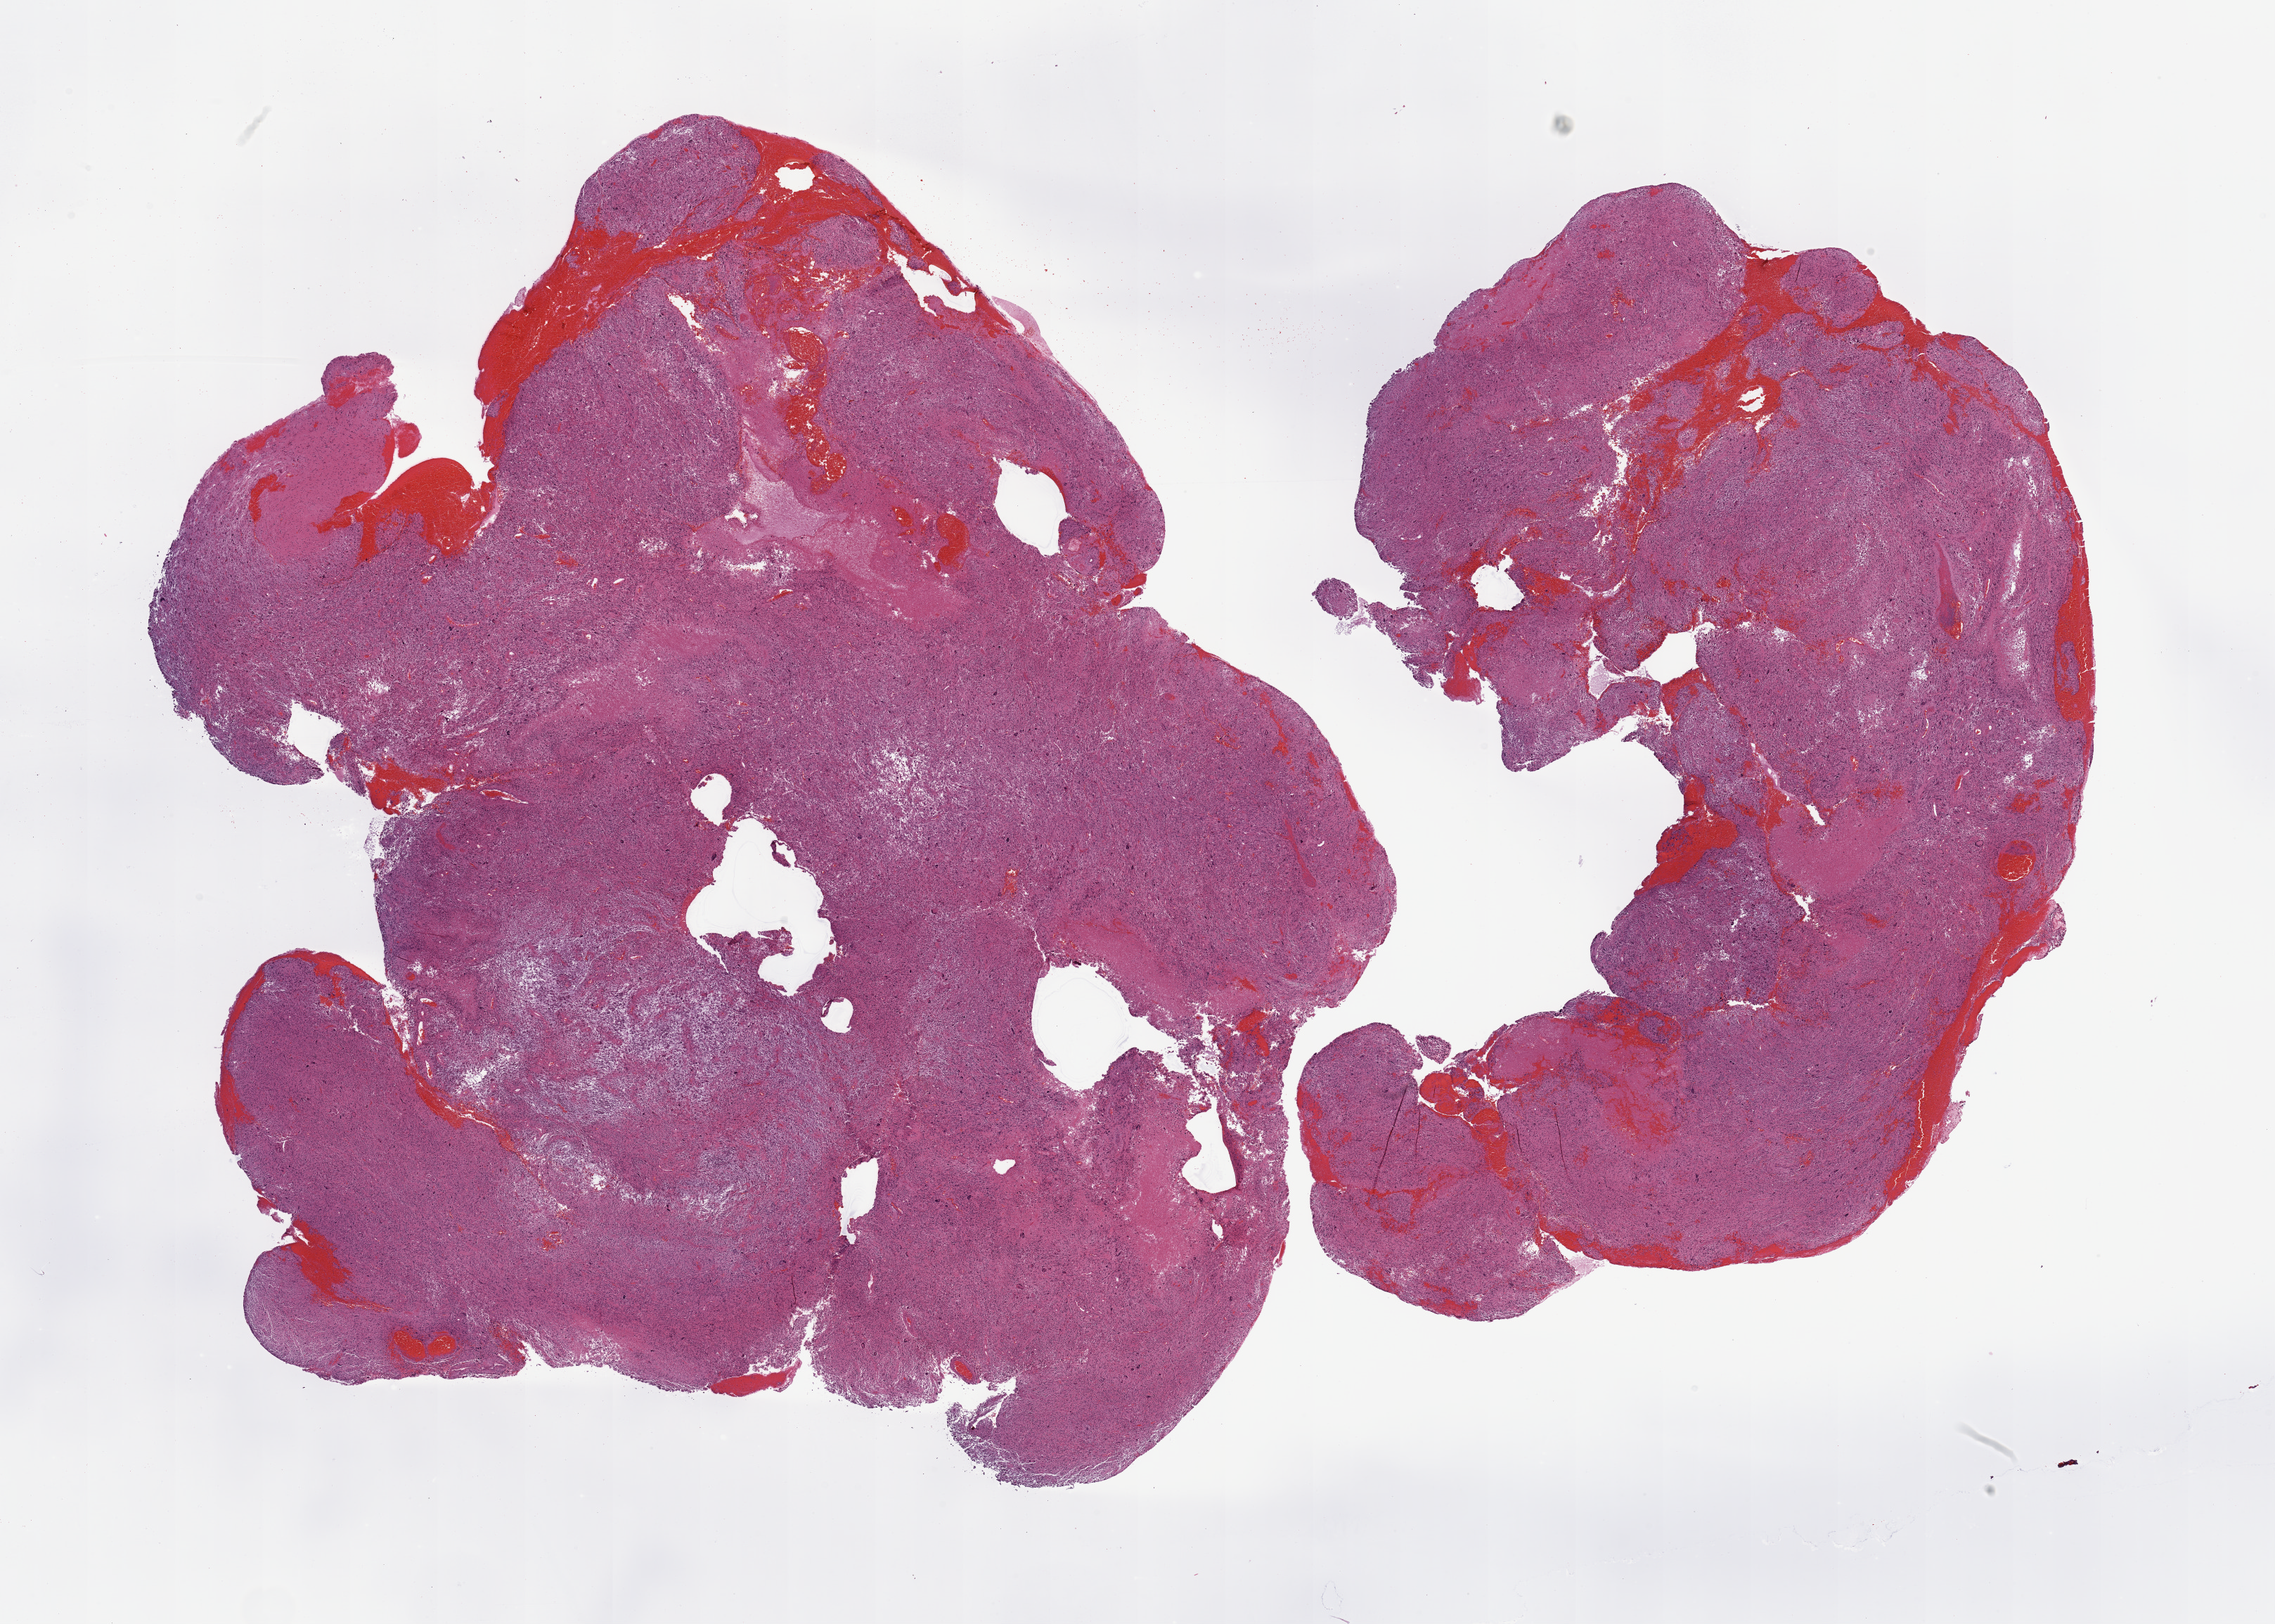
Digitized H&E tissue section (whole slide) — shown as a low-resolution overview of the whole scanned area (about 25.6 x 18.3 mm), tumour tissue sample, sampled site: brain. Male, 43 y/o. Pathologist review of this section (percent, as recorded): tumour nuclei 85%, necrosis 7%.
Primary tumour site (as recorded): parietal lobe. Diagnosis: Glioblastoma.